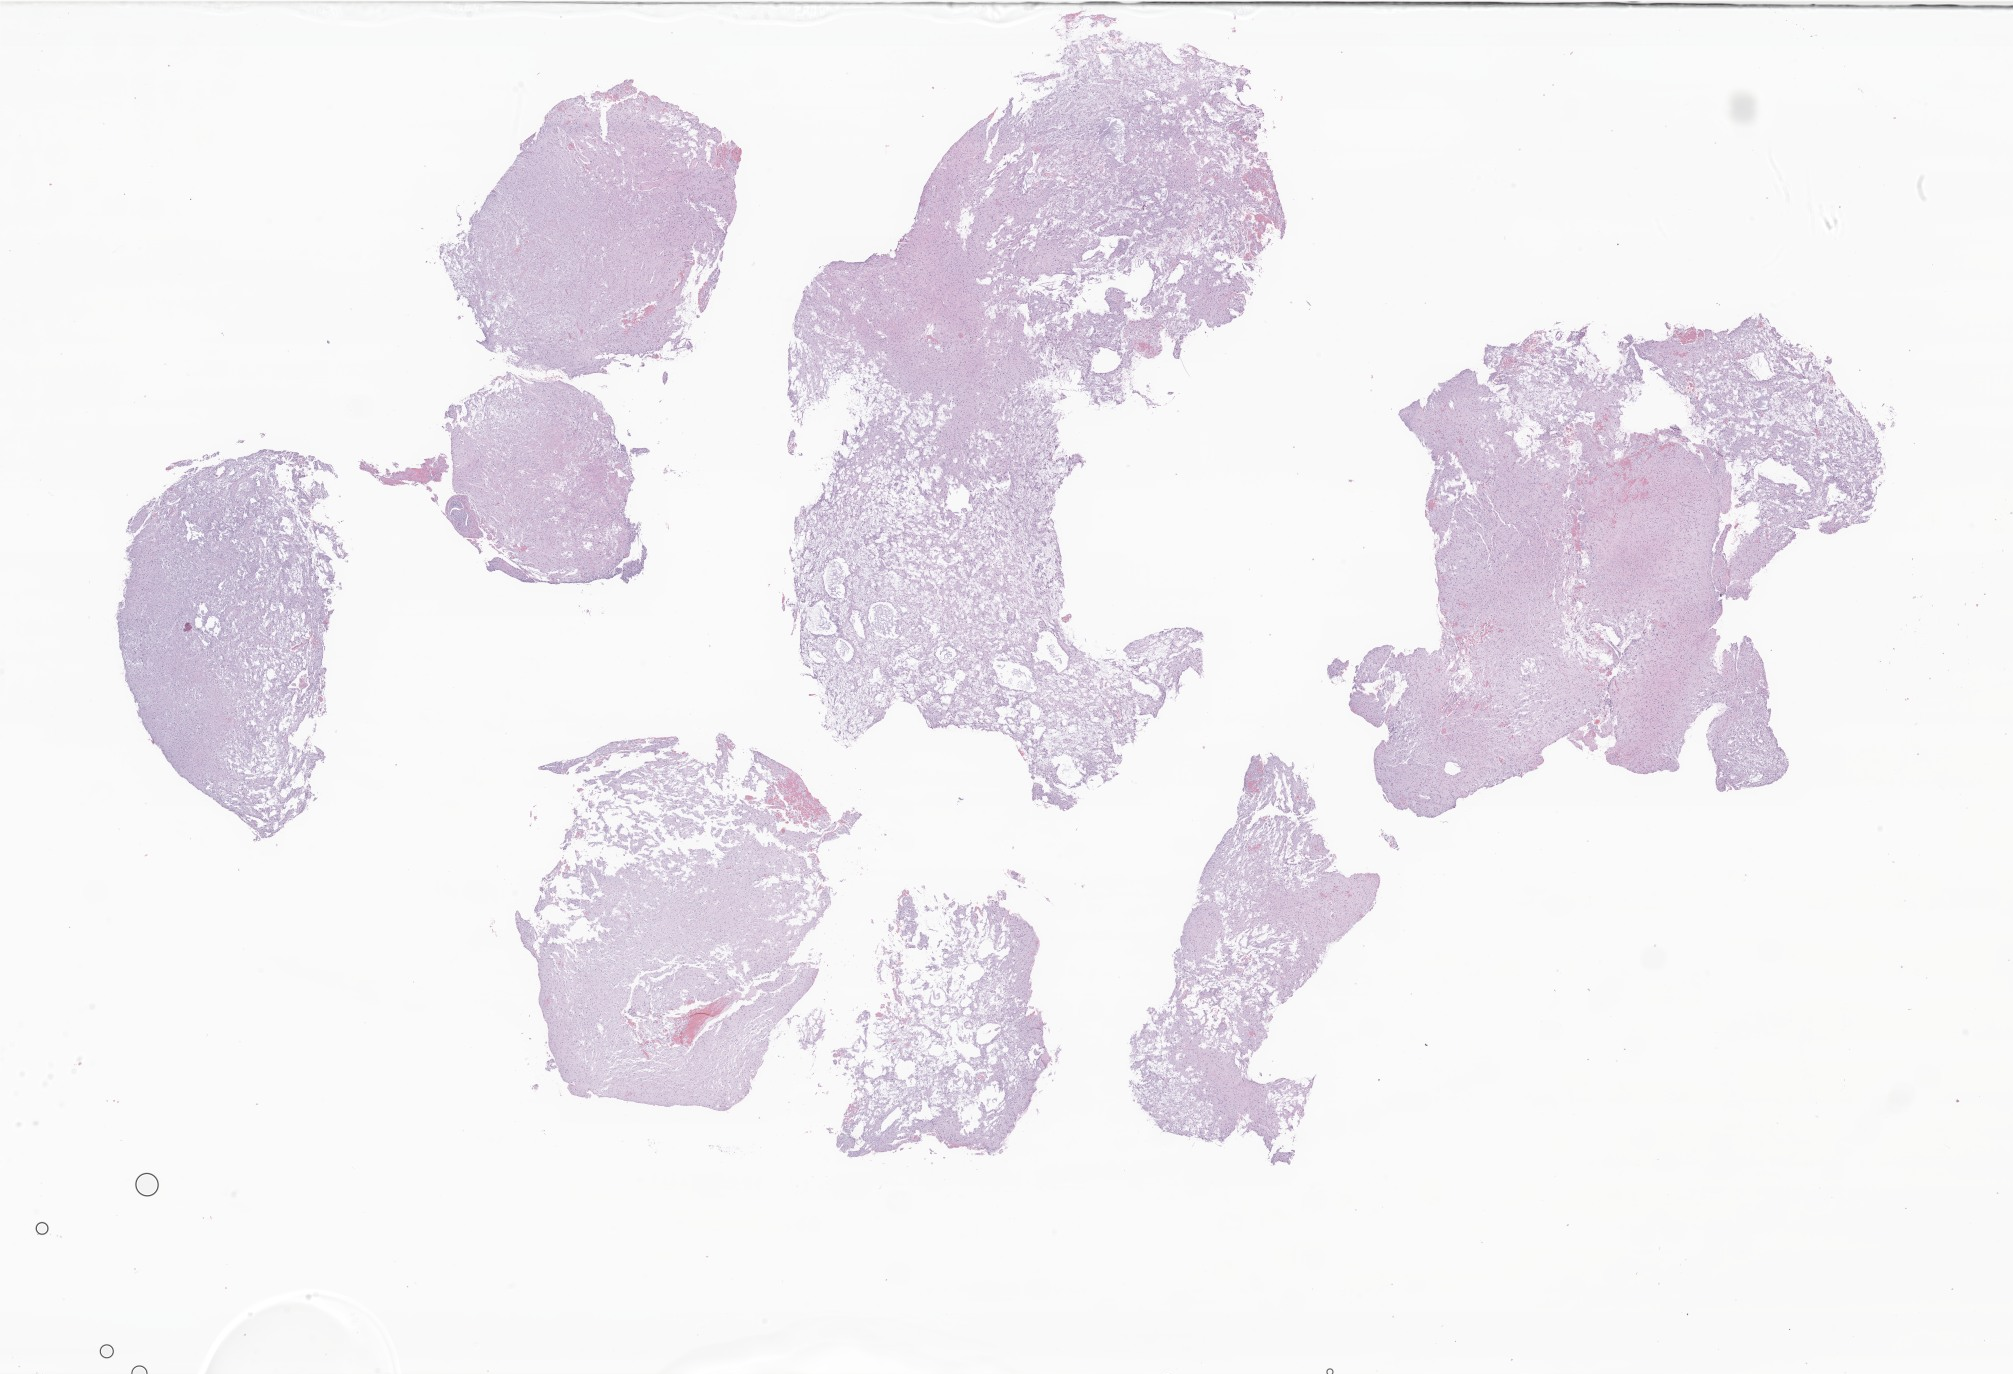
Whole-slide image, haematoxylin and eosin stain of tumor tissue from the cerebellum, a low-resolution overview of the entire scanned area, about 34.0 x 23.2 mm; FFPE section. Male patient, age 127 months.
Diagnosis (ICD-O-3 morphology term): Pilocytic astrocytoma.